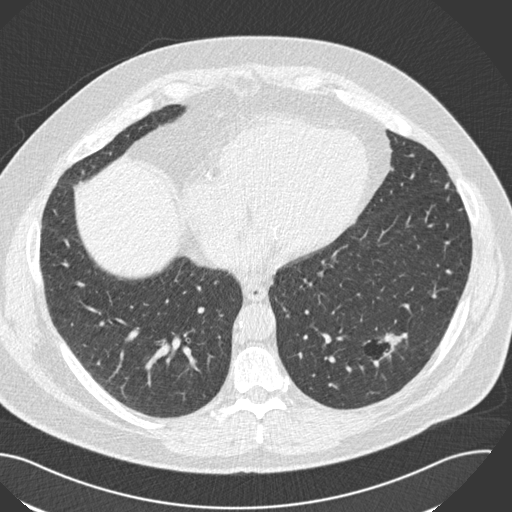
Low-dose screening chest CT, one axial slice; position 65 of 153 along the scan axis; reconstruction kernel B30f; 120 kVp; lung window (W 1500 / L -600 HU); 2 mm slice thickness; 512 × 512 image matrix.
Outlined on this slice (outlined manually by an expert reader):
- lesion 1 (tumor, lower lobe of left lung): bounding box [x1, y1, x2, y2] px = [384, 334, 404, 350]